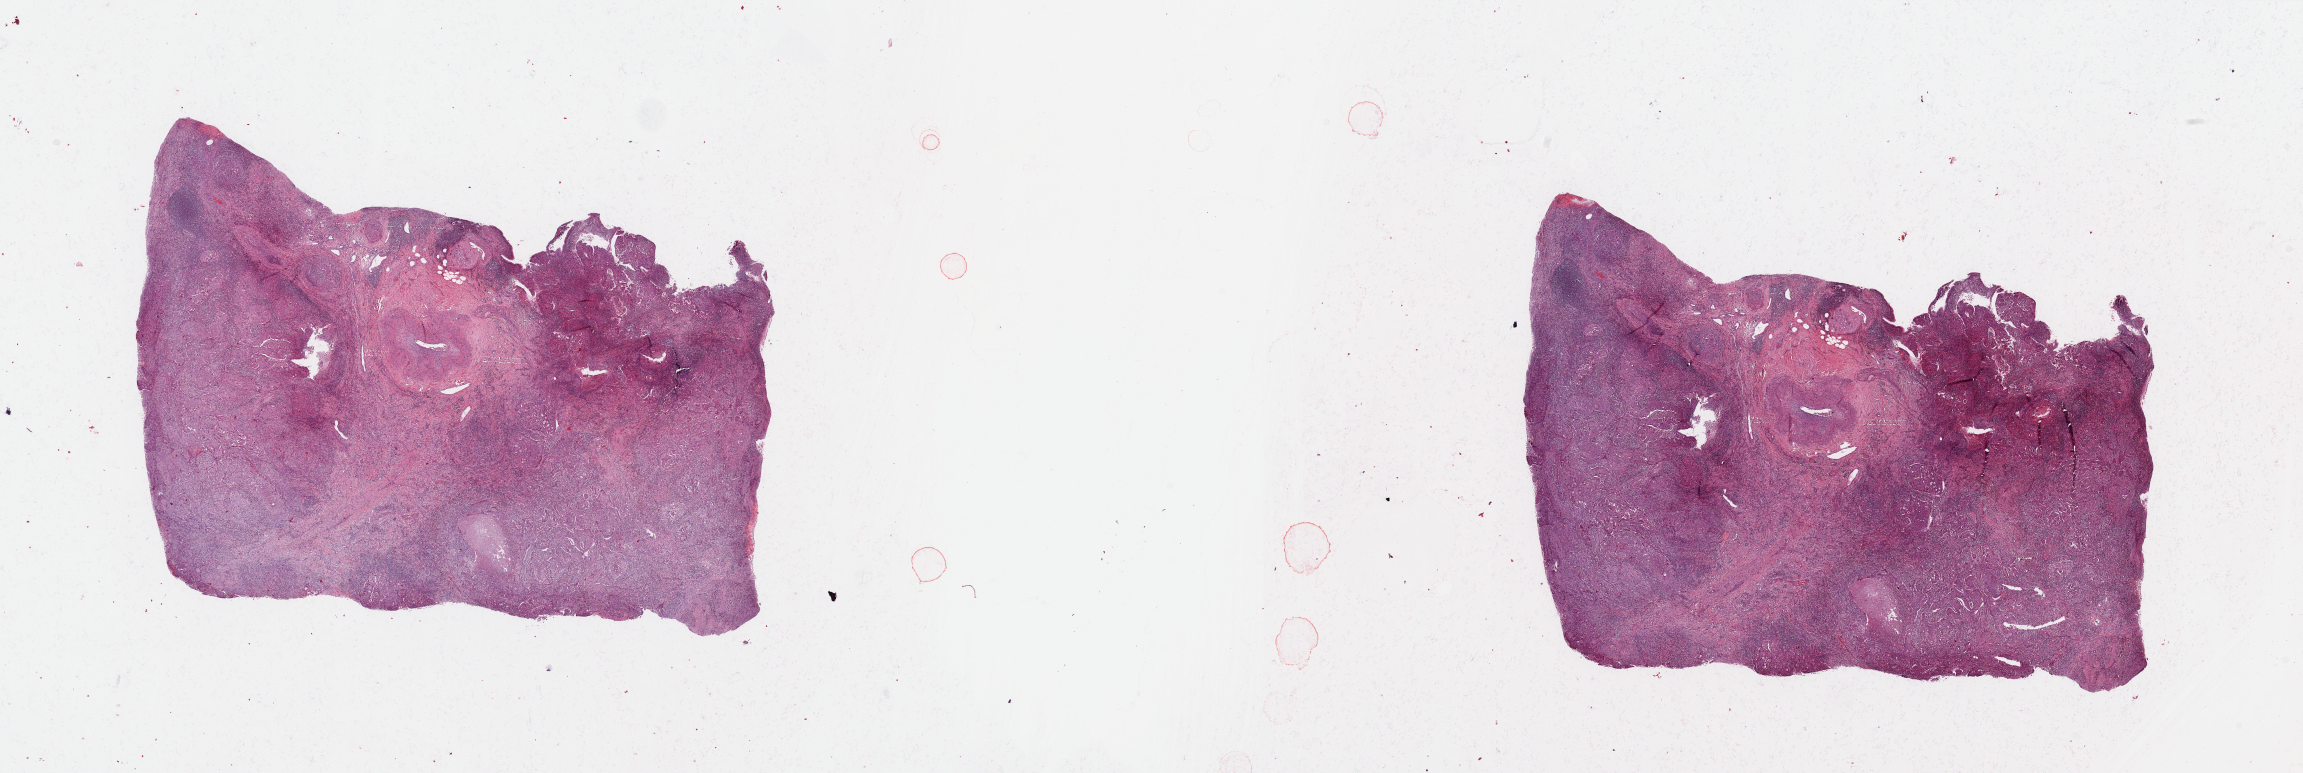
Hematoxylin and eosin (H&E) stained whole-slide image — shown as a low-resolution overview of the whole scanned area (about 36.4 x 12.2 mm, from a 20x scan), tumour tissue sample, sampled site: lung. Male, 57 y/o. Histologic grade: G2 (moderately differentiated). Pathologist review of this section (percent, as recorded): tumour nuclei 65%, necrosis 5%.
- AJCC pathologic stage: IIB
- diagnosis: Squamous cell carcinoma, NOS
- primary tumour site (as recorded): right lower lobe